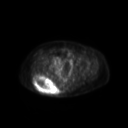
FDG PET of an extremity soft-tissue mass (from a PET/CT study), one axial slice. Slice 60 of 267 in the series (ordered by position). 3.27 mm slice thickness. 128 × 128 image matrix, field of view 600 × 600 mm. Female patient, age 60 years. From the clinical record (not read from this slice): histological type: spindle cell suggestive of myxofibrosarcoma; grade: intermediate; site of the primary tumour: right buttock.
Structures marked on this image (expert contour drawn on MRI and transferred to this co-registered scan by the dataset authors):
- gross tumour volume (mass): bounding box <34,76,59,95> (left, top, right, bottom; pixels)